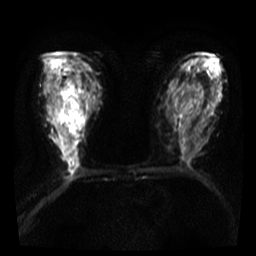
Breast MRI, one axial slice. Diffusion-weighted series; image 2 of 4 stored at this slice position (different b-values; order by instance number). 3 T. 5 mm slice thickness. 256 × 256 image matrix, field of view 300 × 300 mm. Female patient.
Structures marked on this image (outlined manually by an expert reader):
- tumour on diffusion-weighted imaging: bounding box (x1, y1, x2, y2) in pixels: (57, 97, 63, 112)